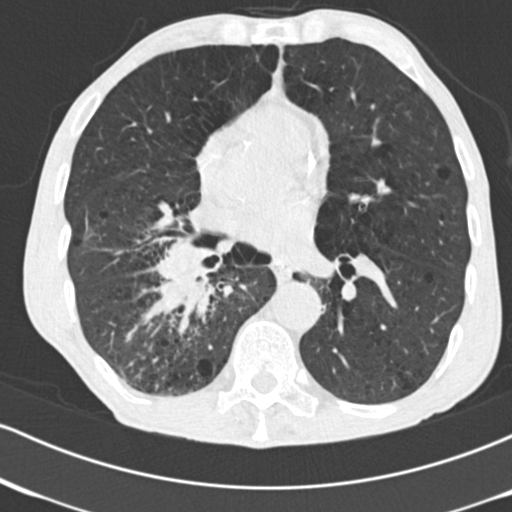
Axial slice from a low-dose chest CT screening exam; second screening round (one year after baseline); lung window (W 1500 / L -600 HU); 2 mm slice thickness; standard (soft-tissue) reconstruction kernel (B30f); slice 104 of 182 in the series; 512 × 512 image matrix, field of view 316 × 316 mm. Male participant, aged 64 years at enrolment.
Lesion marked by an expert reader, bounding box [x1, y1, x2, y2] px = [125, 225, 242, 336]. The exam's reader record, not a measurement of the box and not confirmed to be the same lesion: non-calcified nodule or mass ≥4 mm, 52 × 37 mm, spiculated (stellate) margins, soft tissue attenuation, pre-existing on the prior screen: no. Official screen result: positive, other. Later outcome: lung cancer diagnosed 28 days after this screen — adenocarcinoma, NOS, right lower lobe, stage IV (AJCC 6th edition), 60 mm at pathology.